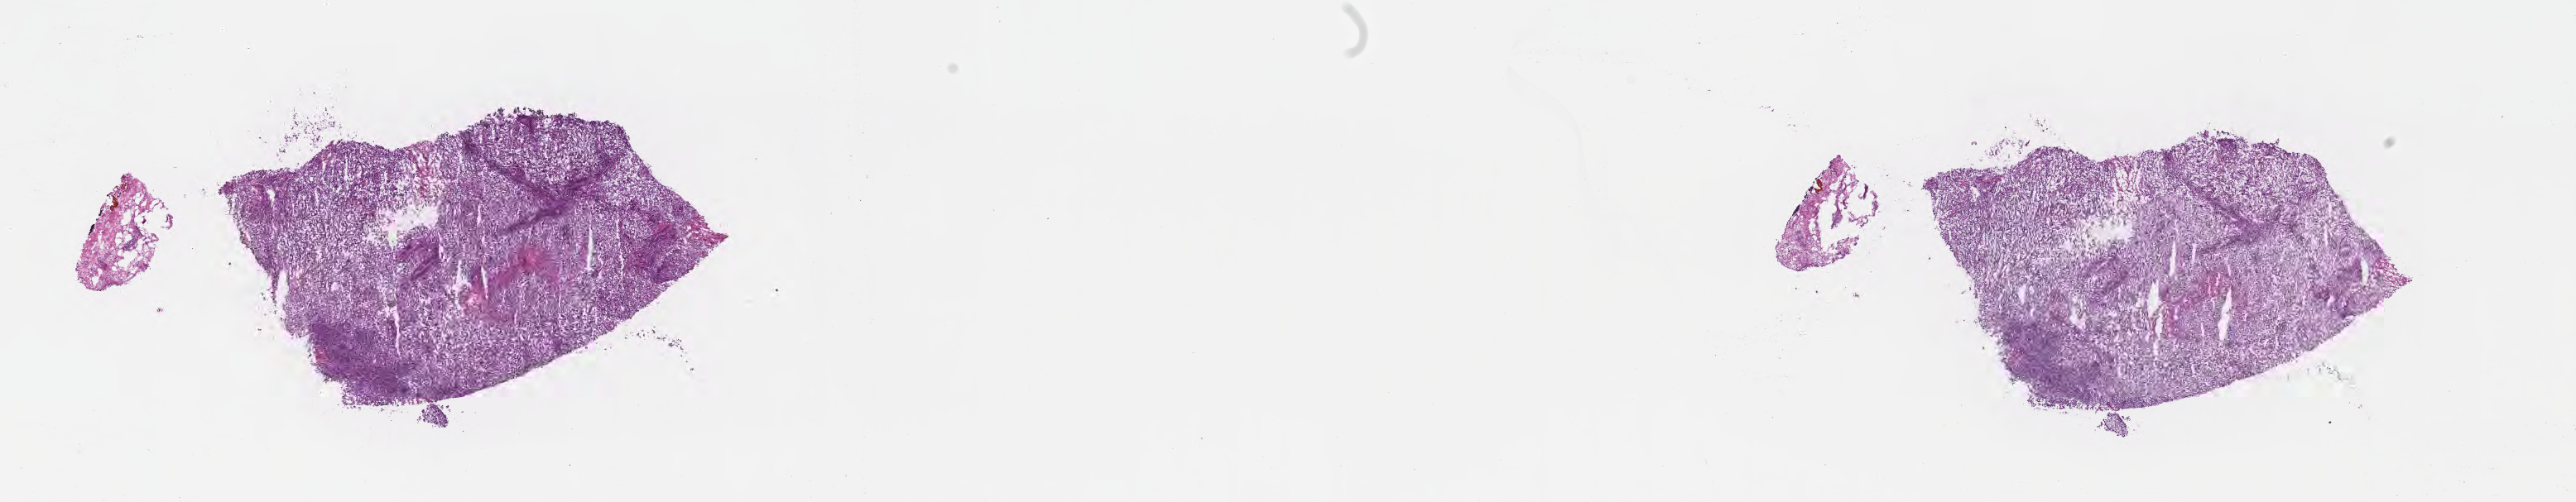
Hematoxylin and eosin (H&E) whole-slide image, a low-resolution overview of the entire scanned area, about 25.2 x 4.9 mm. Cryosection. Metastatic tumor tissue, resected from lymph node. Patient: male, age at initial diagnosis 53 years. Pathologist review of this section (percent, as recorded): tumor cells 54%, tumor nuclei 60%, stromal cells 40%, necrosis 6%, normal cells 0%. Inflammatory infiltration, as recorded: lymphocyte infiltration 35%, monocyte infiltration 1%, neutrophil infiltration 0%.
Patient diagnosis (primary): Malignant melanoma, NOS.